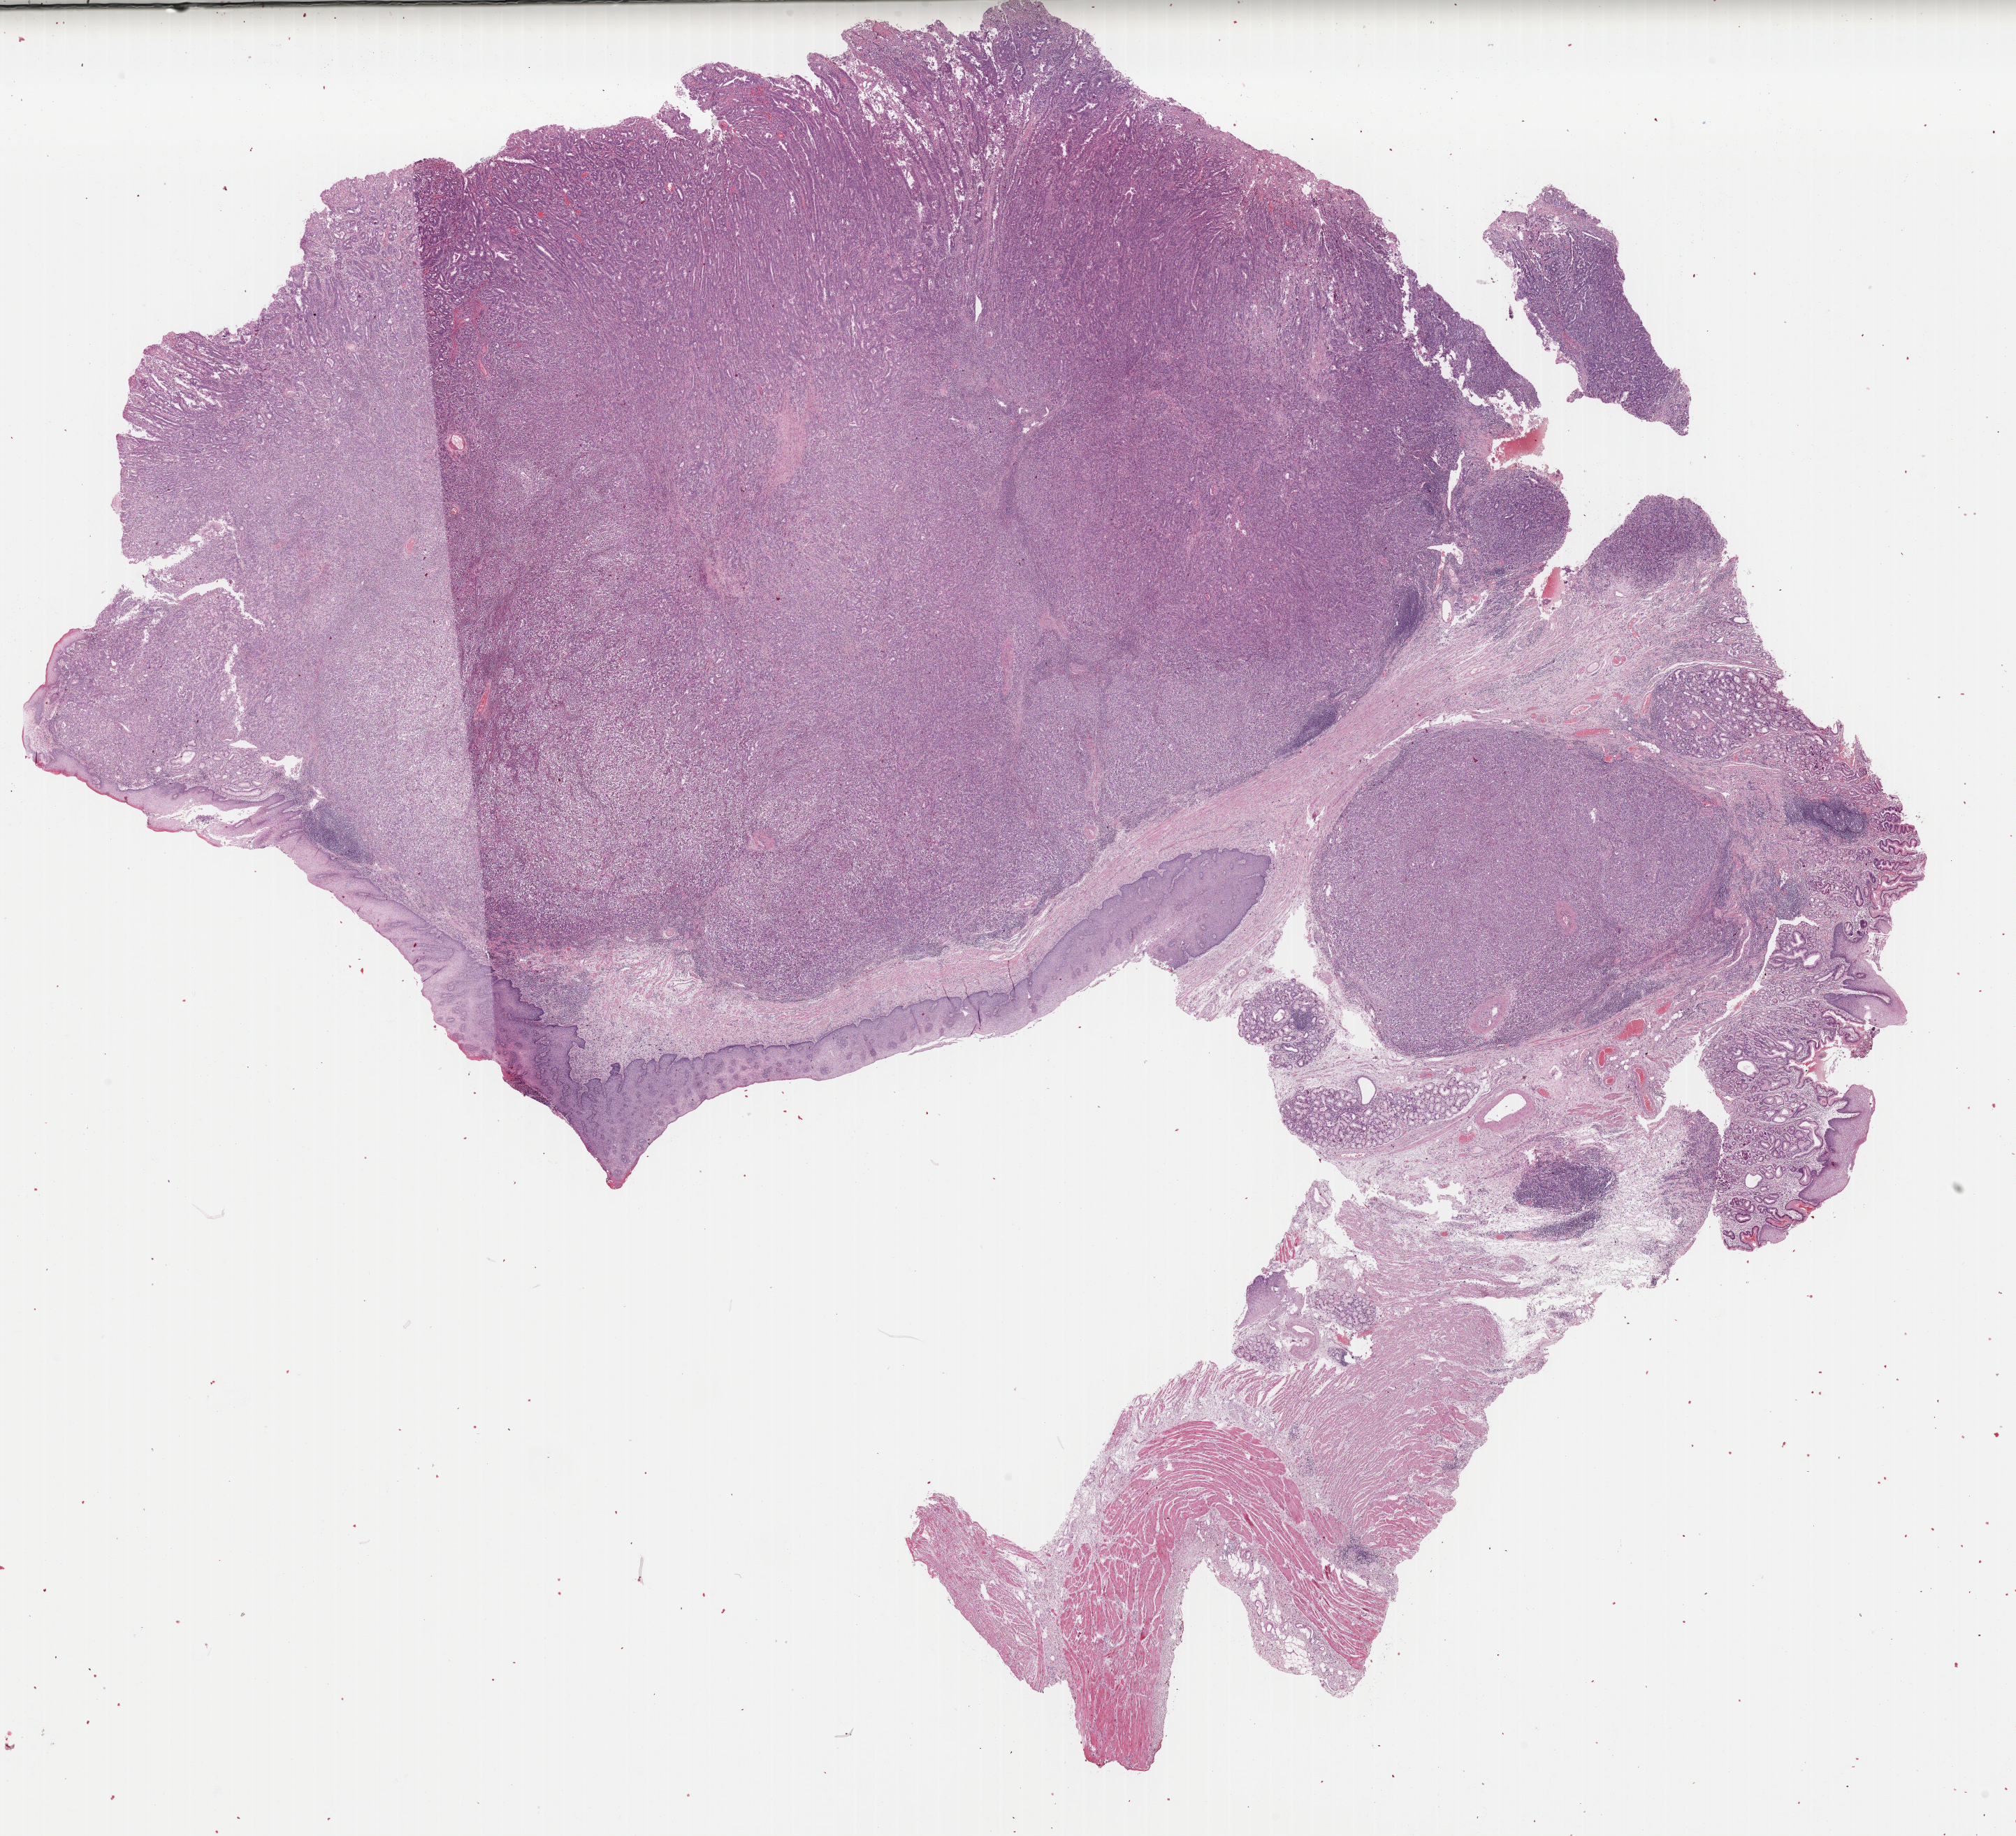
Whole-slide histology image, H&E, whole scanned area (about 22.8 x 20.7 mm, slide scanned at 40x) shown as a low-resolution overview. Formalin-fixed paraffin-embedded (FFPE) diagnostic section. Sample: primary tumour, stomach. Male patient; age at initial diagnosis 44 years. Histologic grade: G3 (poorly differentiated).
TNM: T3 N3a M0. Lymph nodes positive (case pathology): 13 of 24 examined. Diagnosis: Tubular adenocarcinoma. AJCC pathologic stage: IIIB (7th edition).